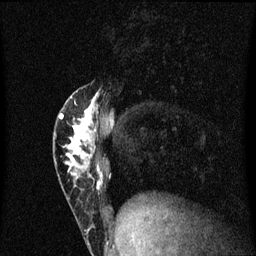
Breast MRI (dynamic contrast-enhanced), one sagittal slice. Position 20 of 60 along the scan axis. Dynamic contrast-enhanced series, image 2 of 3 at this slice position (ordered by acquisition). 1.5 T. TE 4.2 ms, TR 8.4 ms. 2 mm slice thickness. 256 × 256 image matrix, field of view 200 × 200 mm. Female patient, age 40 years.
Structures marked on this image (semi-automatically segmented with operator editing):
- analysis volume of interest (the breast-tissue region the enhancement analysis was run in; not a lesion): bounding box [x1, y1, x2, y2] px = [54, 88, 105, 203]
- tumour enhancement mask (voxels above the 70 % enhancement threshold inside the analysis volume of interest): [59, 94, 100, 179]